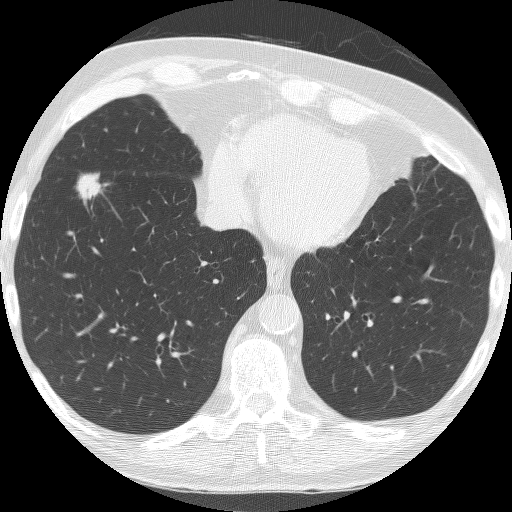
Chest CT (low-dose screening protocol), one axial image. Baseline screening round. Lung window (W 1500 / L -600 HU). Lung (sharp) reconstruction kernel (BONE). 120 kVp. 512 × 512 image matrix, field of view 320 × 320 mm. Male, age 74 years at enrolment. Former smoker at enrolment.
• Expert-annotated lung lesion, bounding box (x1, y1, x2, y2) in pixels: (69, 166, 119, 206).
• The screening reader recorded 4 non-calcified nodules or masses ≥4 mm on this exam (right lower lobe, right lower lobe, right lower lobe, right lower lobe); which of them this box marks is not recorded.
• Participant outcome: lung cancer diagnosed 35 days after this screen — bronchiolo-alveolar carcinoma, mucinous, right lower lobe, well differentiated (G1), stage IA (AJCC 6th edition), 22 mm at pathology.